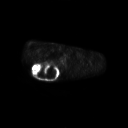
FDG PET of an extremity soft-tissue mass (from a PET/CT study), one axial slice; position 200 of 267 along the scan axis; 3.27 mm slice thickness; 128 × 128 image matrix, field of view 700 × 700 mm. Male patient, age 61 years. From the clinical record (not read from this slice): histological type: pleiomorphic spindle cell undifferentiated; grade: high; site of the primary tumour: right parascapusular.
Structures marked on this image (expert contour drawn on MRI and transferred to this co-registered scan by the dataset authors):
- gross tumour volume including surrounding oedema: bounding box (x1, y1, x2, y2) in pixels: (32, 62, 60, 78)
- gross tumour volume (mass): (32, 63, 58, 78)